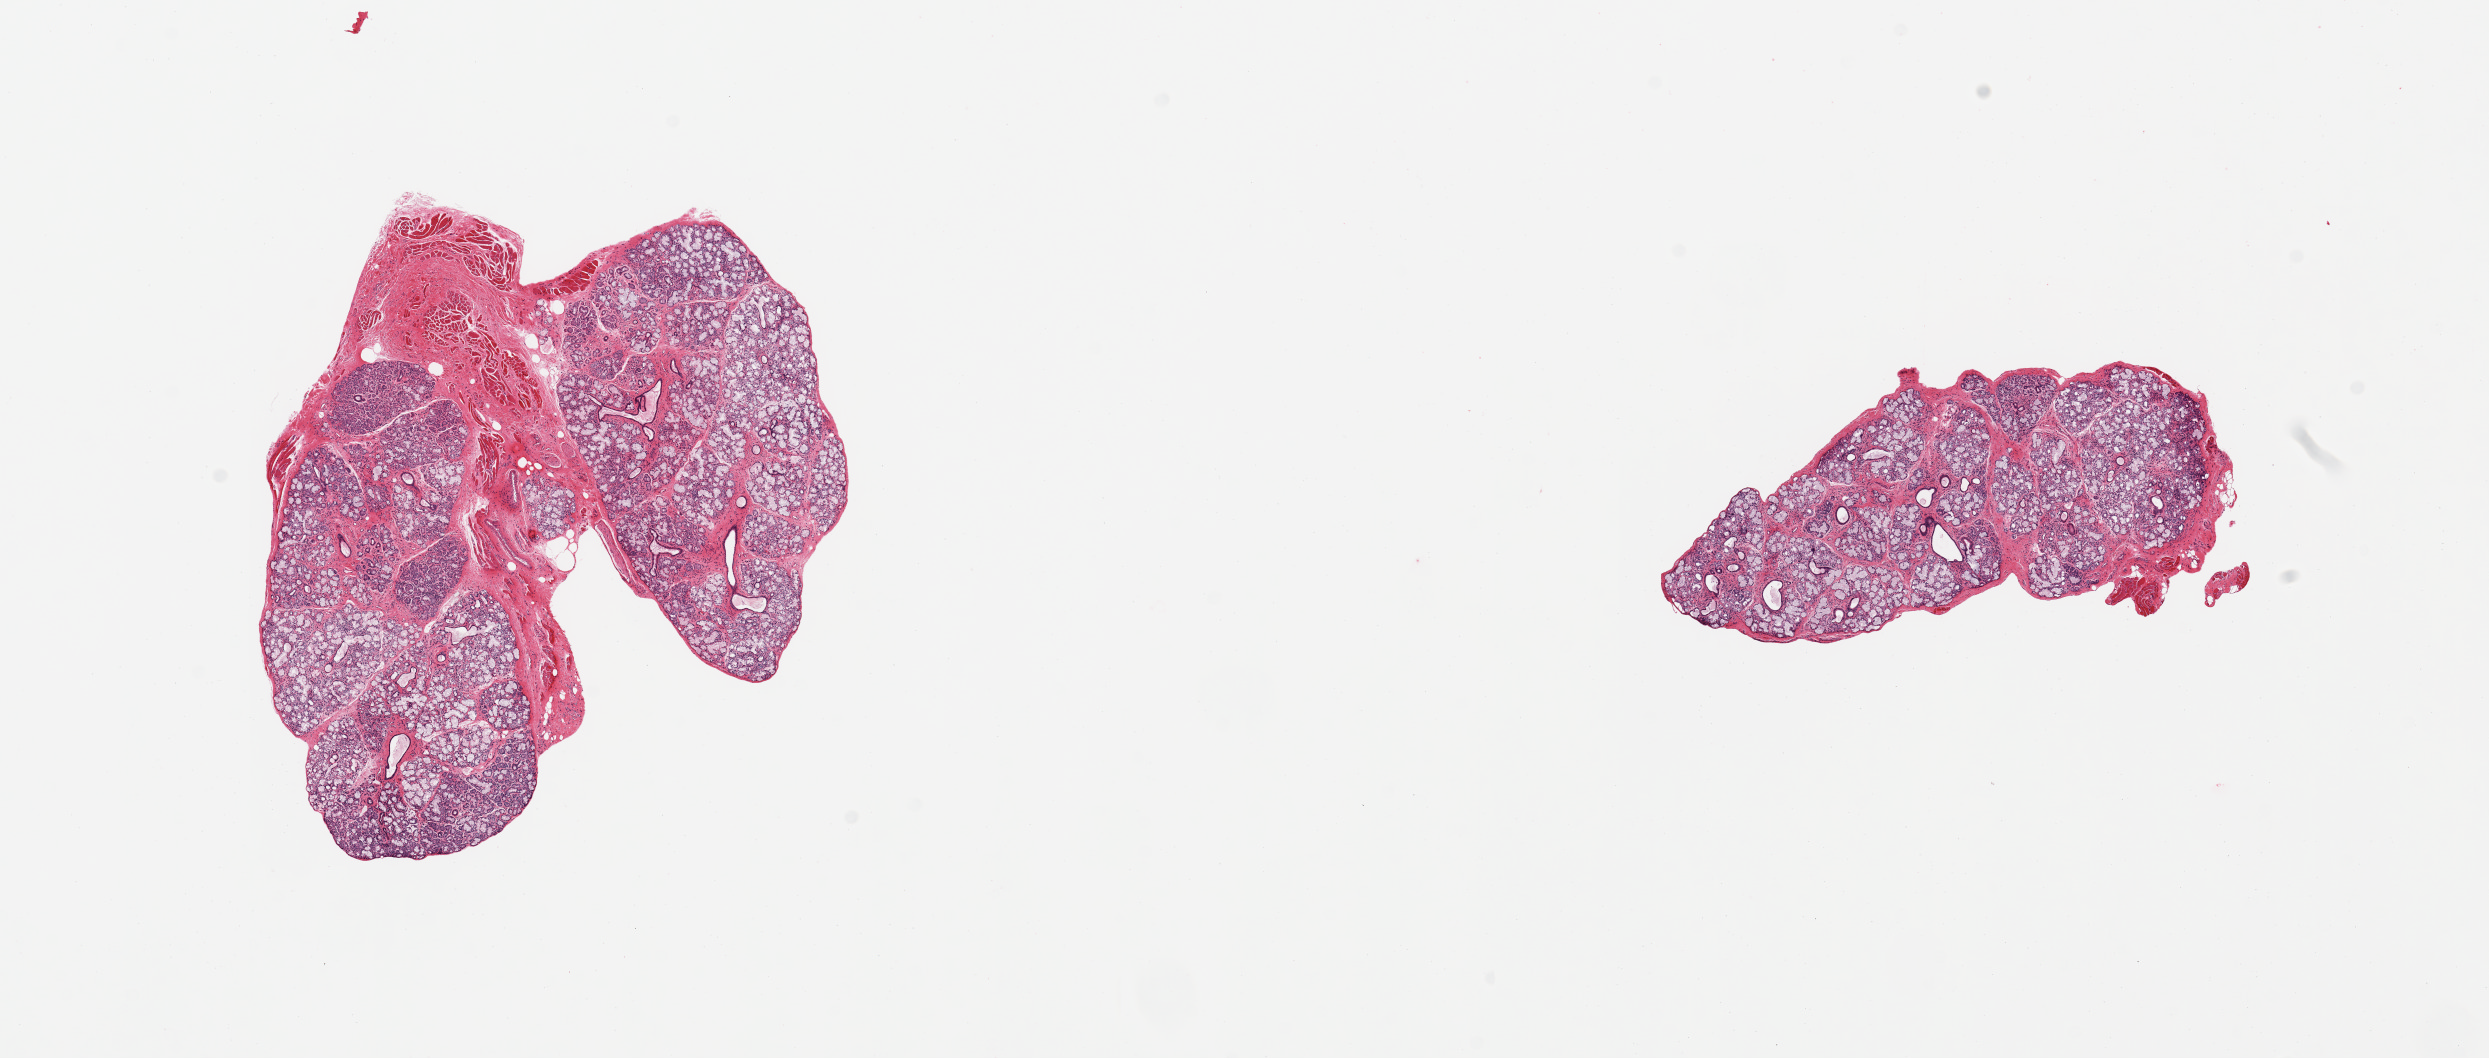
Digitized H&E-stained section — low-resolution overview of the scanned area, about 19.7 x 8.4 mm. PAXgene-fixed paraffin-embedded (PFPE) section. Sampled site (target tissue): minor salivary gland. Donor tissue sample. Donor: male.
Pathologist's review note for this sample: 2 pieces; well dissected except for adherent fibromuscular tissue between 2 glands, 1.2x1.5mm.